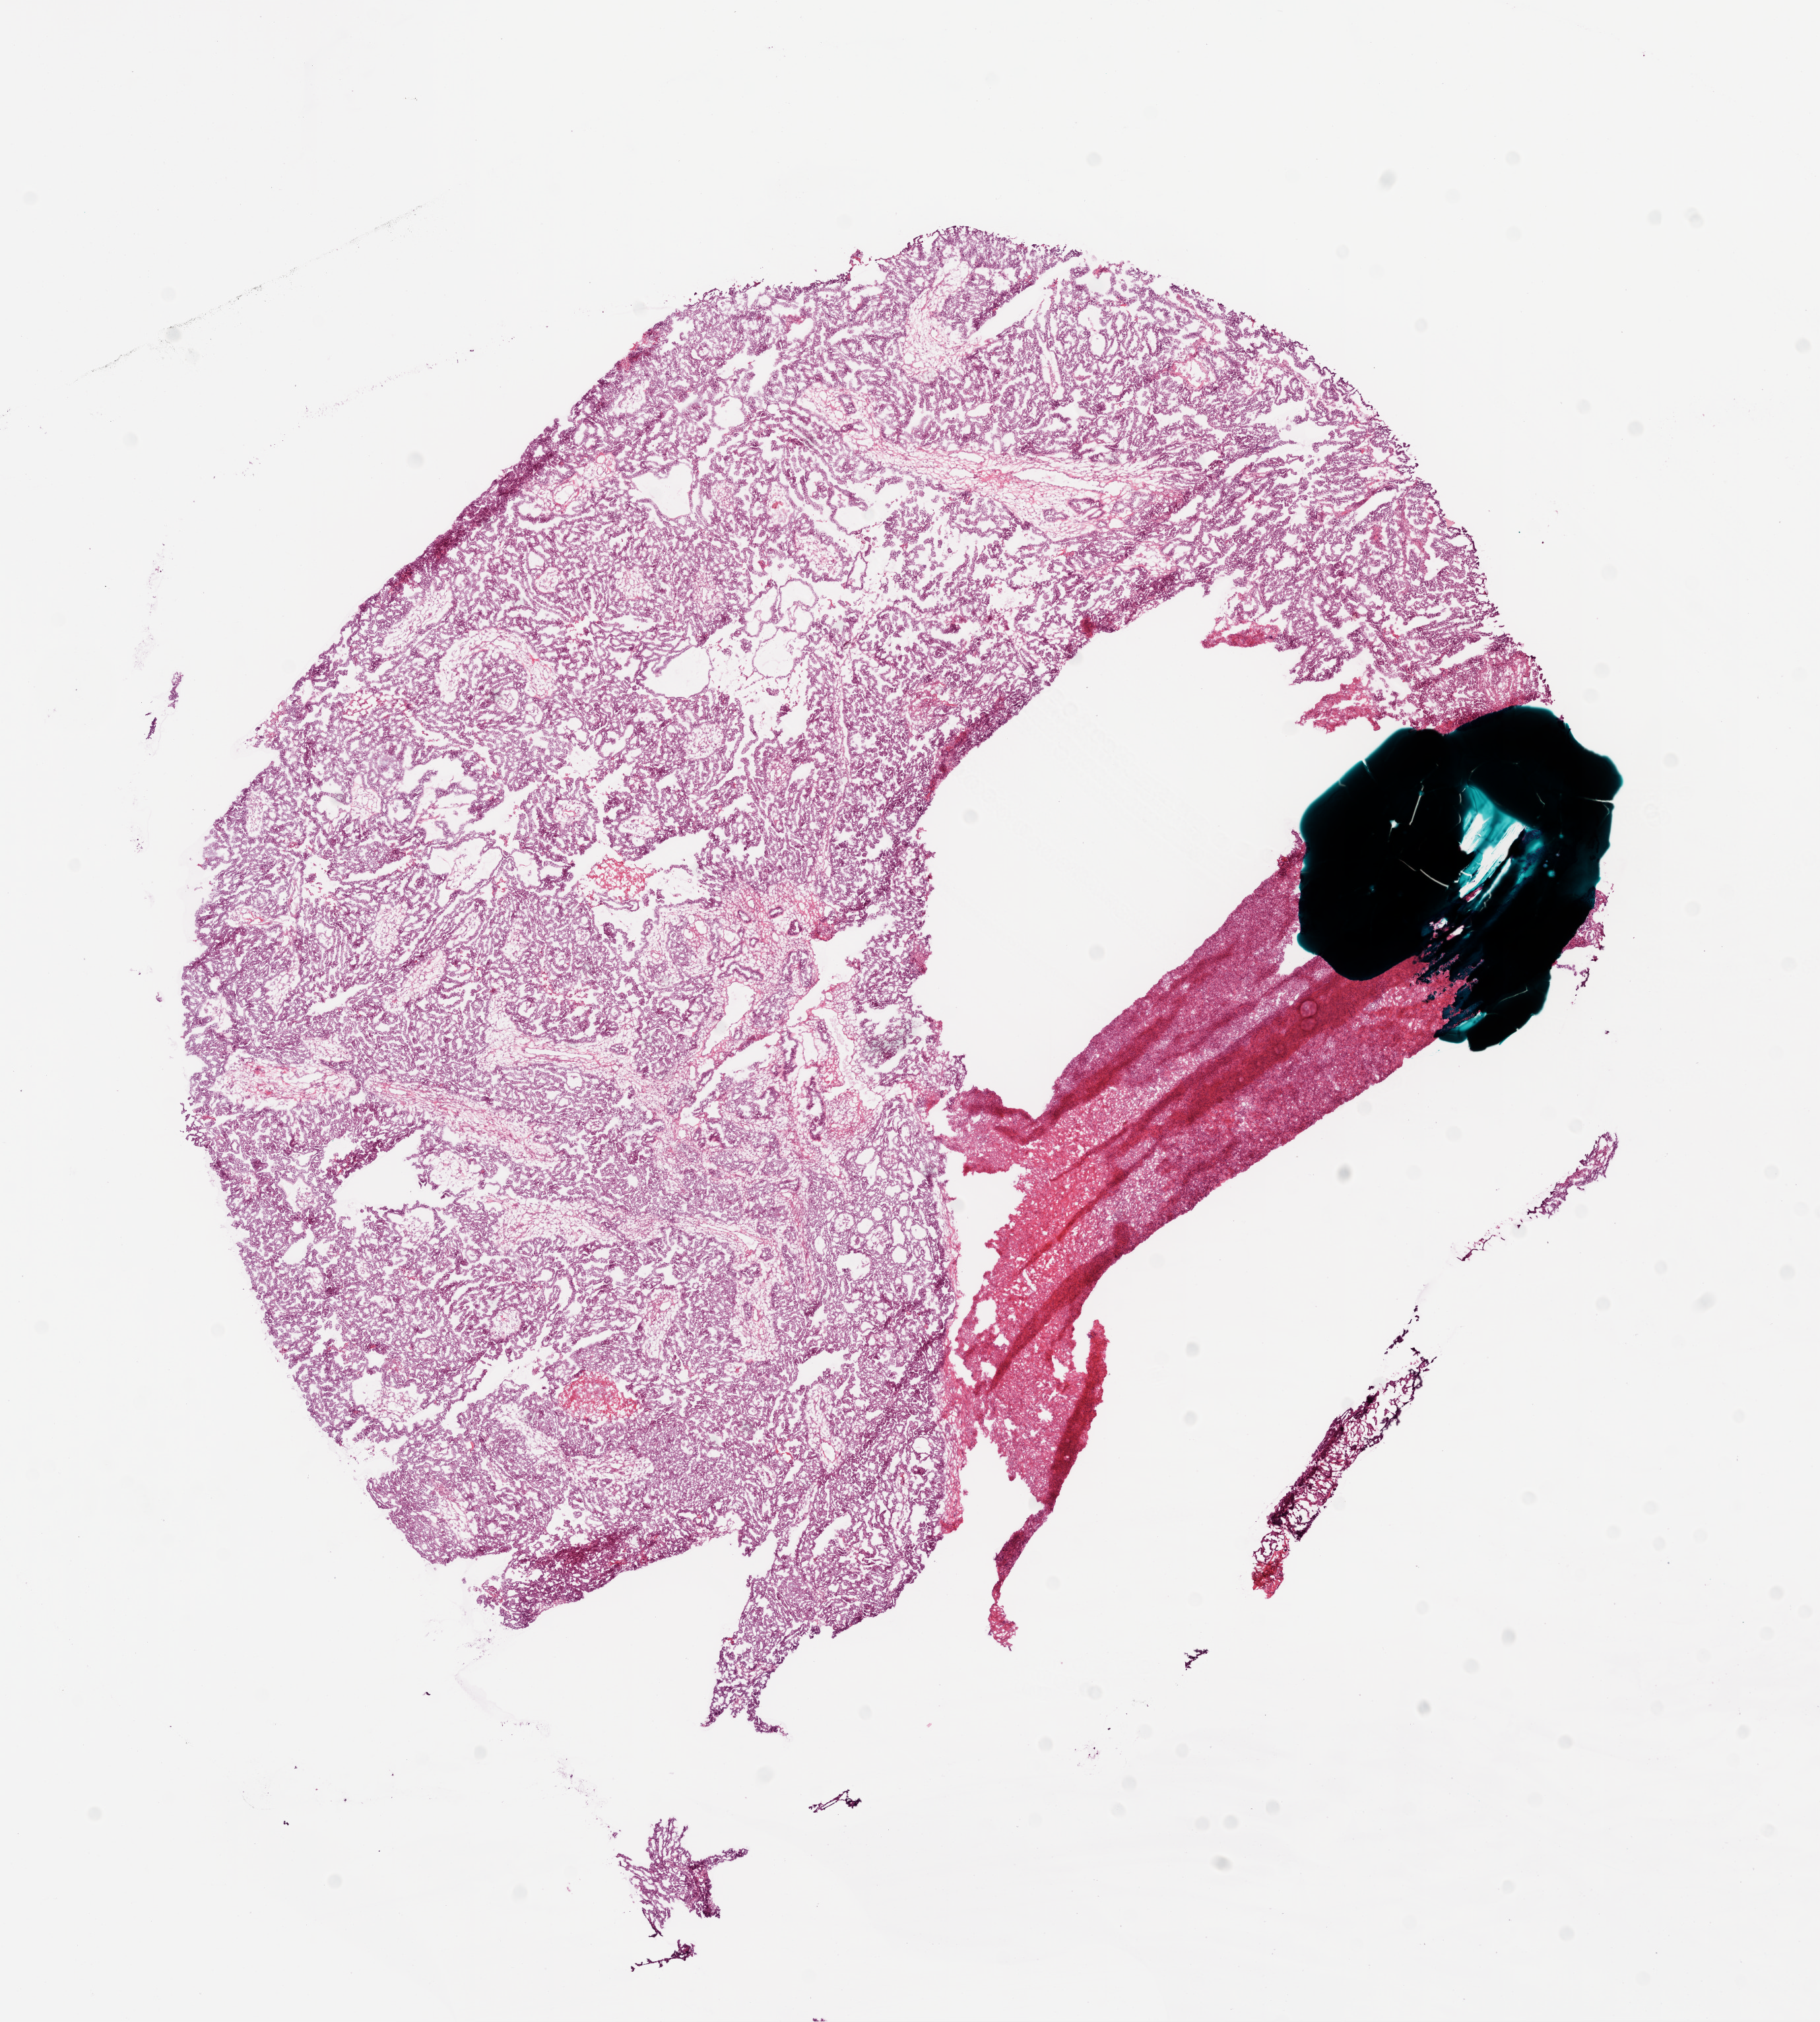
Whole-slide histology image, H&E, whole scanned area (about 11.1 x 12.4 mm, from a 20x scan) shown as a low-resolution overview. Frozen section. Ovary, primary tumour sample. Female patient; age at initial diagnosis 67 years. Histologic grade: G3 (poorly differentiated). Pathologist review of this section (percent, as recorded): tumour cells 90%, tumour nuclei 90%, normal cells 5%, stromal cells 5%, necrosis 0%.
* histologic diagnosis: Serous cystadenocarcinoma, NOS
* FIGO stage: IIIC